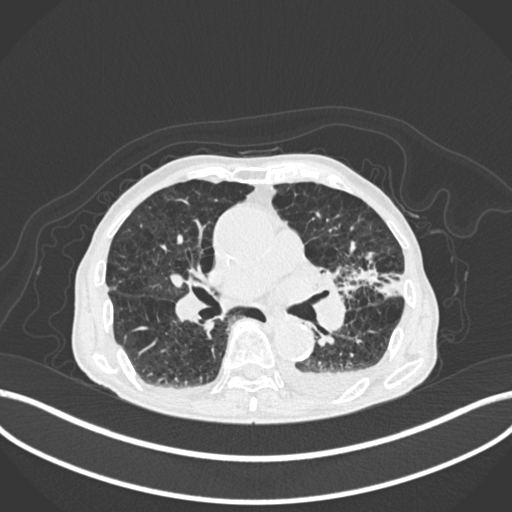
Chest CT, one axial slice; slice 118 of 400 in the series (ordered by position); 120 kVp; lung window (W 1500 / L -600 HU); 1 mm slice thickness; 512 × 512 image matrix, field of view 400 × 400 mm. Male patient, age 90 years or older. Case-level facts recorded for this patient, not image findings: clinical TNM (as recorded): T2b N1 M0.
Outlined on this slice (rectangle marked by the reading radiologist):
- lung tumour (recorded histology: squamous cell carcinoma): bounding box <345,261,383,296> (left, top, right, bottom; pixels)